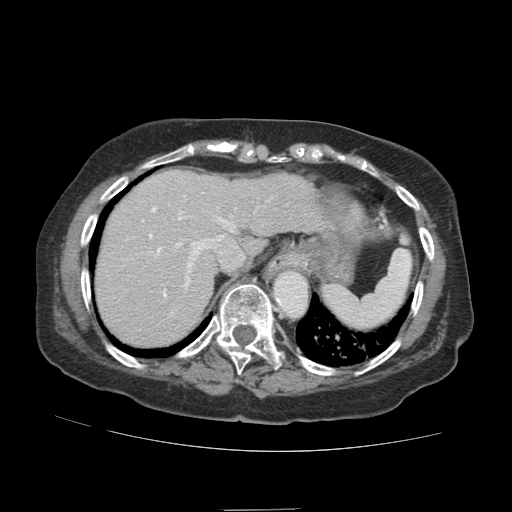
Contrast-enhanced abdominal CT (liver protocol), one axial slice; slice 72 of 89 in the series (ordered by position); reconstruction kernel STANDARD; soft-tissue window (W 400 / L 40 HU); 512 × 512 image matrix, field of view 360 × 360 mm. From the clinical record (not read from this slice): diagnosis: hepatocellular carcinoma (patient treated with transarterial chemoembolisation; whether this scan precedes or follows treatment is not stated here); TNM stage (as recorded): Stage-II; Child-Pugh class: A; tumour differentiation: moderately differentiated; tumour nodularity: multinodular.
Outlined on this slice (semi-automatic segmentation, software-assisted and operator-edited):
- abdominal aorta: bounding box <275,272,308,314> (left, top, right, bottom; pixels)
- liver parenchyma outside the tumour (the mass and vessels are separate outlines, so this box may not span the whole liver): <95,170,361,346>
- liver vessels: <142,192,243,298>